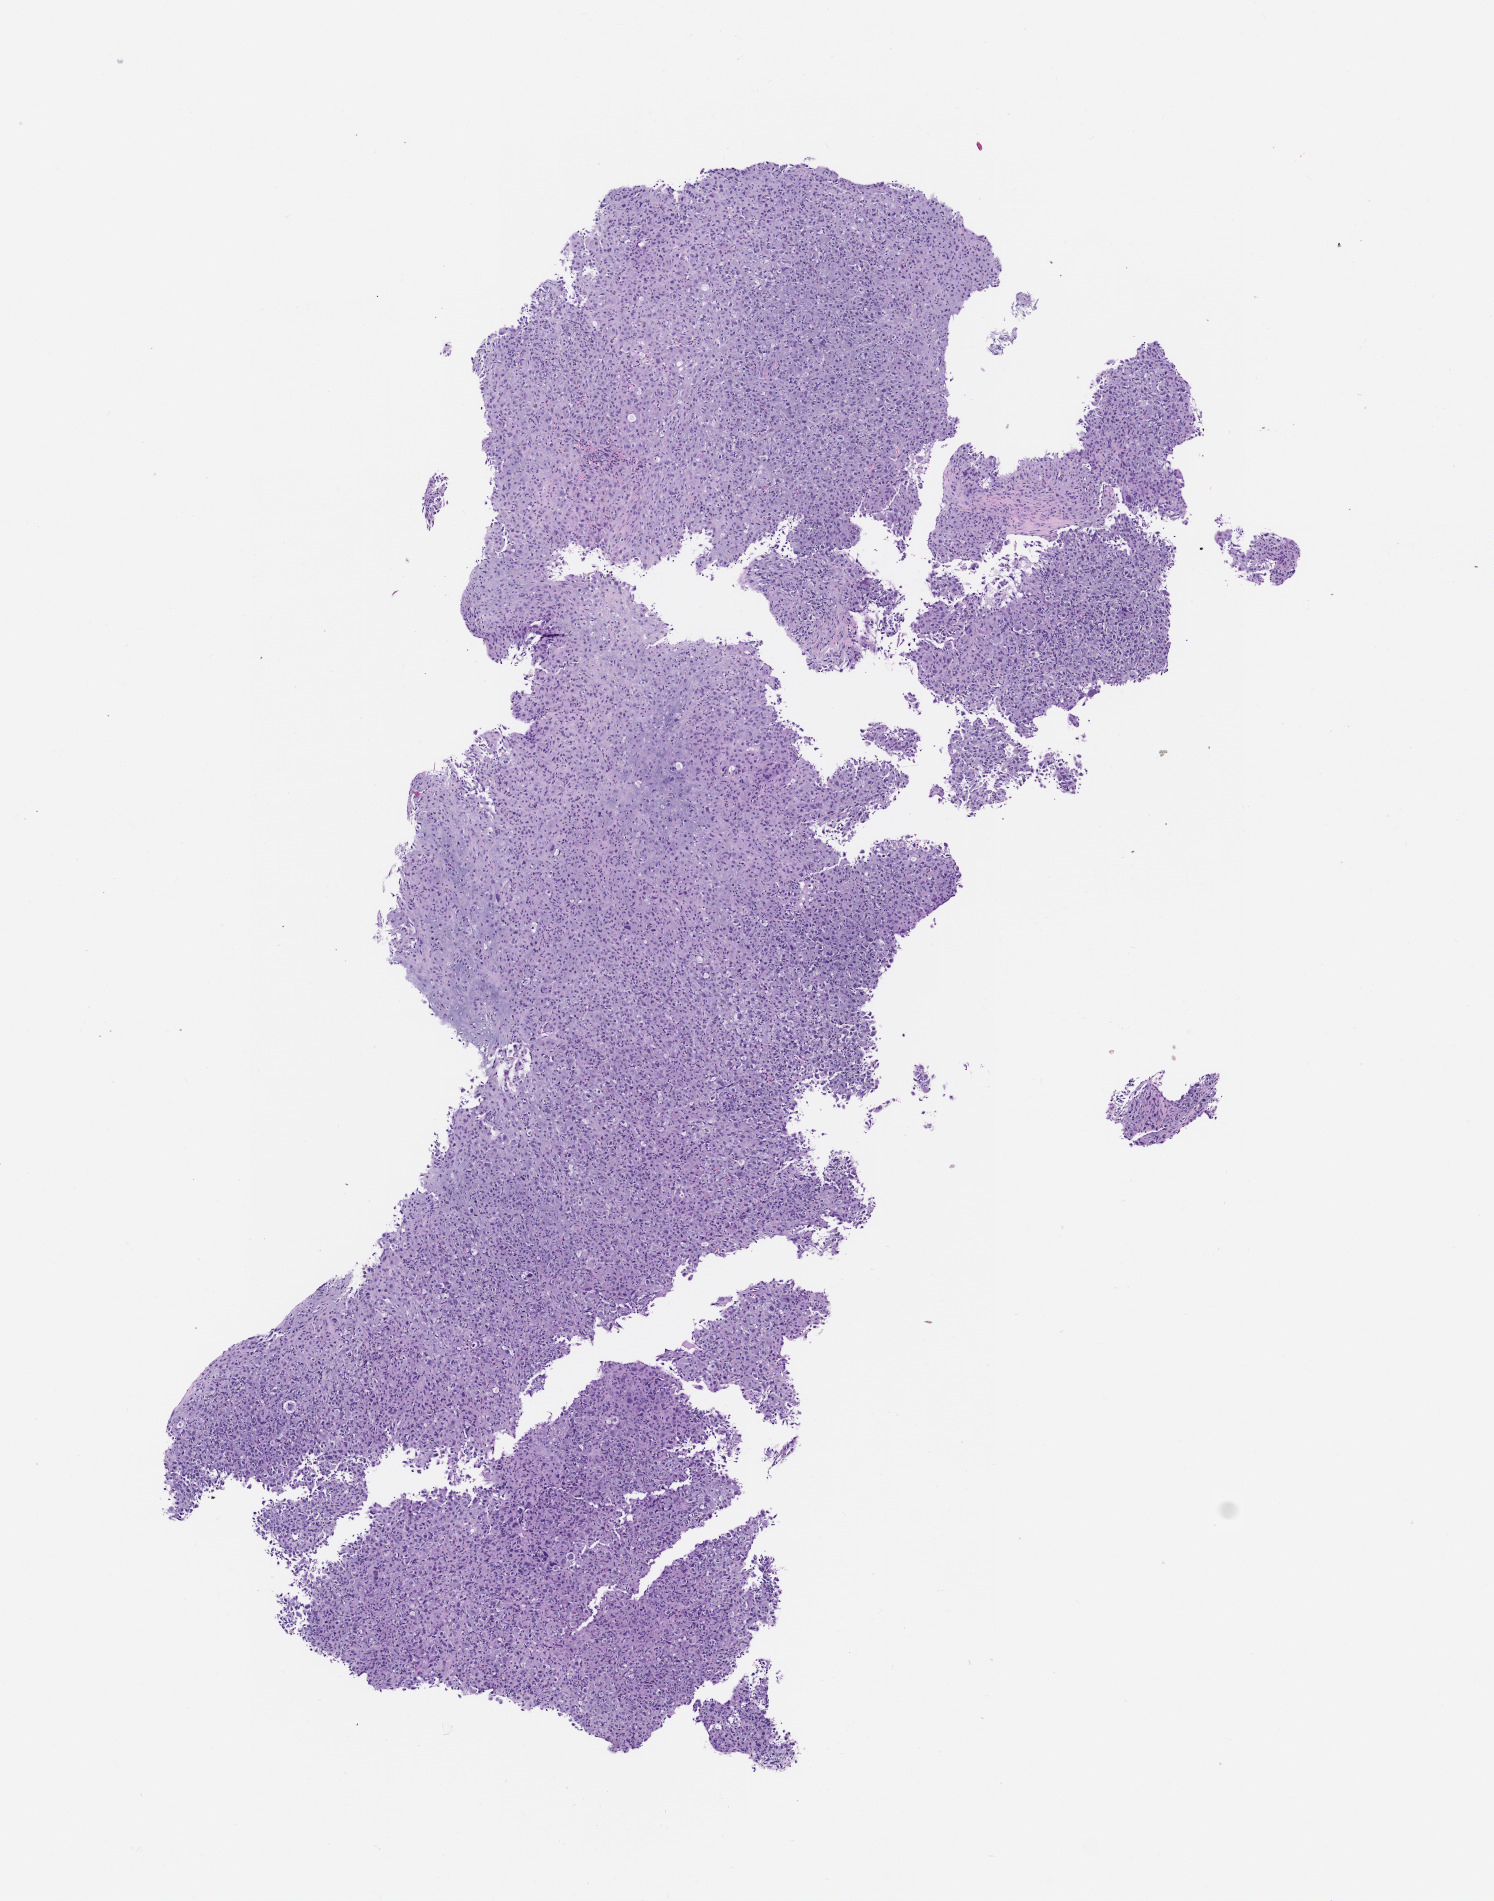
Haematoxylin and eosin whole-slide image of a patient-derived xenograft (PDX) tumor grown in a mouse, passage 1 — low-resolution overview of the scanned area, about 6.0 x 7.6 mm, formalin-fixed, paraffin-embedded (FFPE) tissue, originating tumor site category: bone.
Originating patient diagnosis: Osteosarcoma.